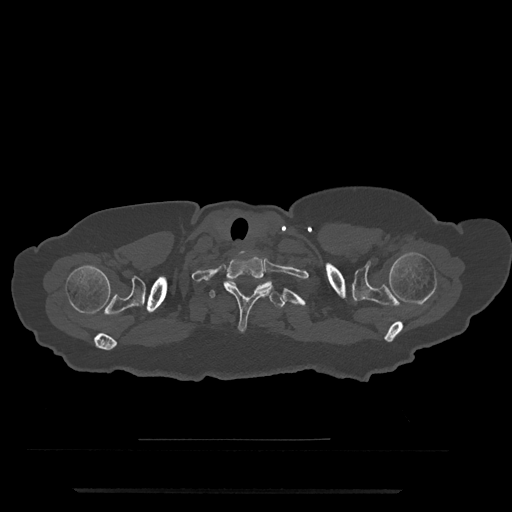
CT including the spine, one axial slice. Position 702 of 797 along the scan axis. Bone window (W 1800 / L 400 HU). 0.5 mm slice thickness. 512 × 512 image matrix, field of view 440 × 440 mm. Patient: female, 51 years. From the clinical record (not read from this slice): primary cancer: neuro.
Outlined on this slice (semi-automatic segmentation, software-assisted and operator-edited):
- T1 vertebra: bounding box (x1, y1, x2, y2) in pixels: (223, 256, 274, 332)
- T2 vertebra: (209, 279, 286, 309)